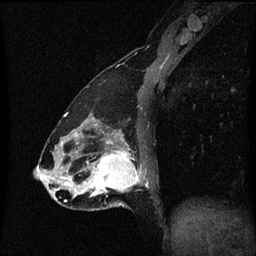
Breast MRI (dynamic contrast-enhanced), one sagittal slice; position 23 of 60 along the scan axis; dynamic contrast-enhanced series, image 2 of 3 at this slice position (ordered by acquisition); 1.5 T; TE 4.2 ms, TR 8.4 ms; 2 mm slice thickness; 256 × 256 image matrix, field of view 200 × 200 mm. Patient: female, 47 years.
Annotated regions visible in this slice (semi-automatic segmentation, software-assisted and operator-edited):
- analysis volume of interest (the breast-tissue region the enhancement analysis was run in; not a lesion): bounding box <81,138,149,211> (left, top, right, bottom; pixels)
- tumour enhancement mask (voxels above the 70 % enhancement threshold inside the analysis volume of interest): <83,138,141,197>